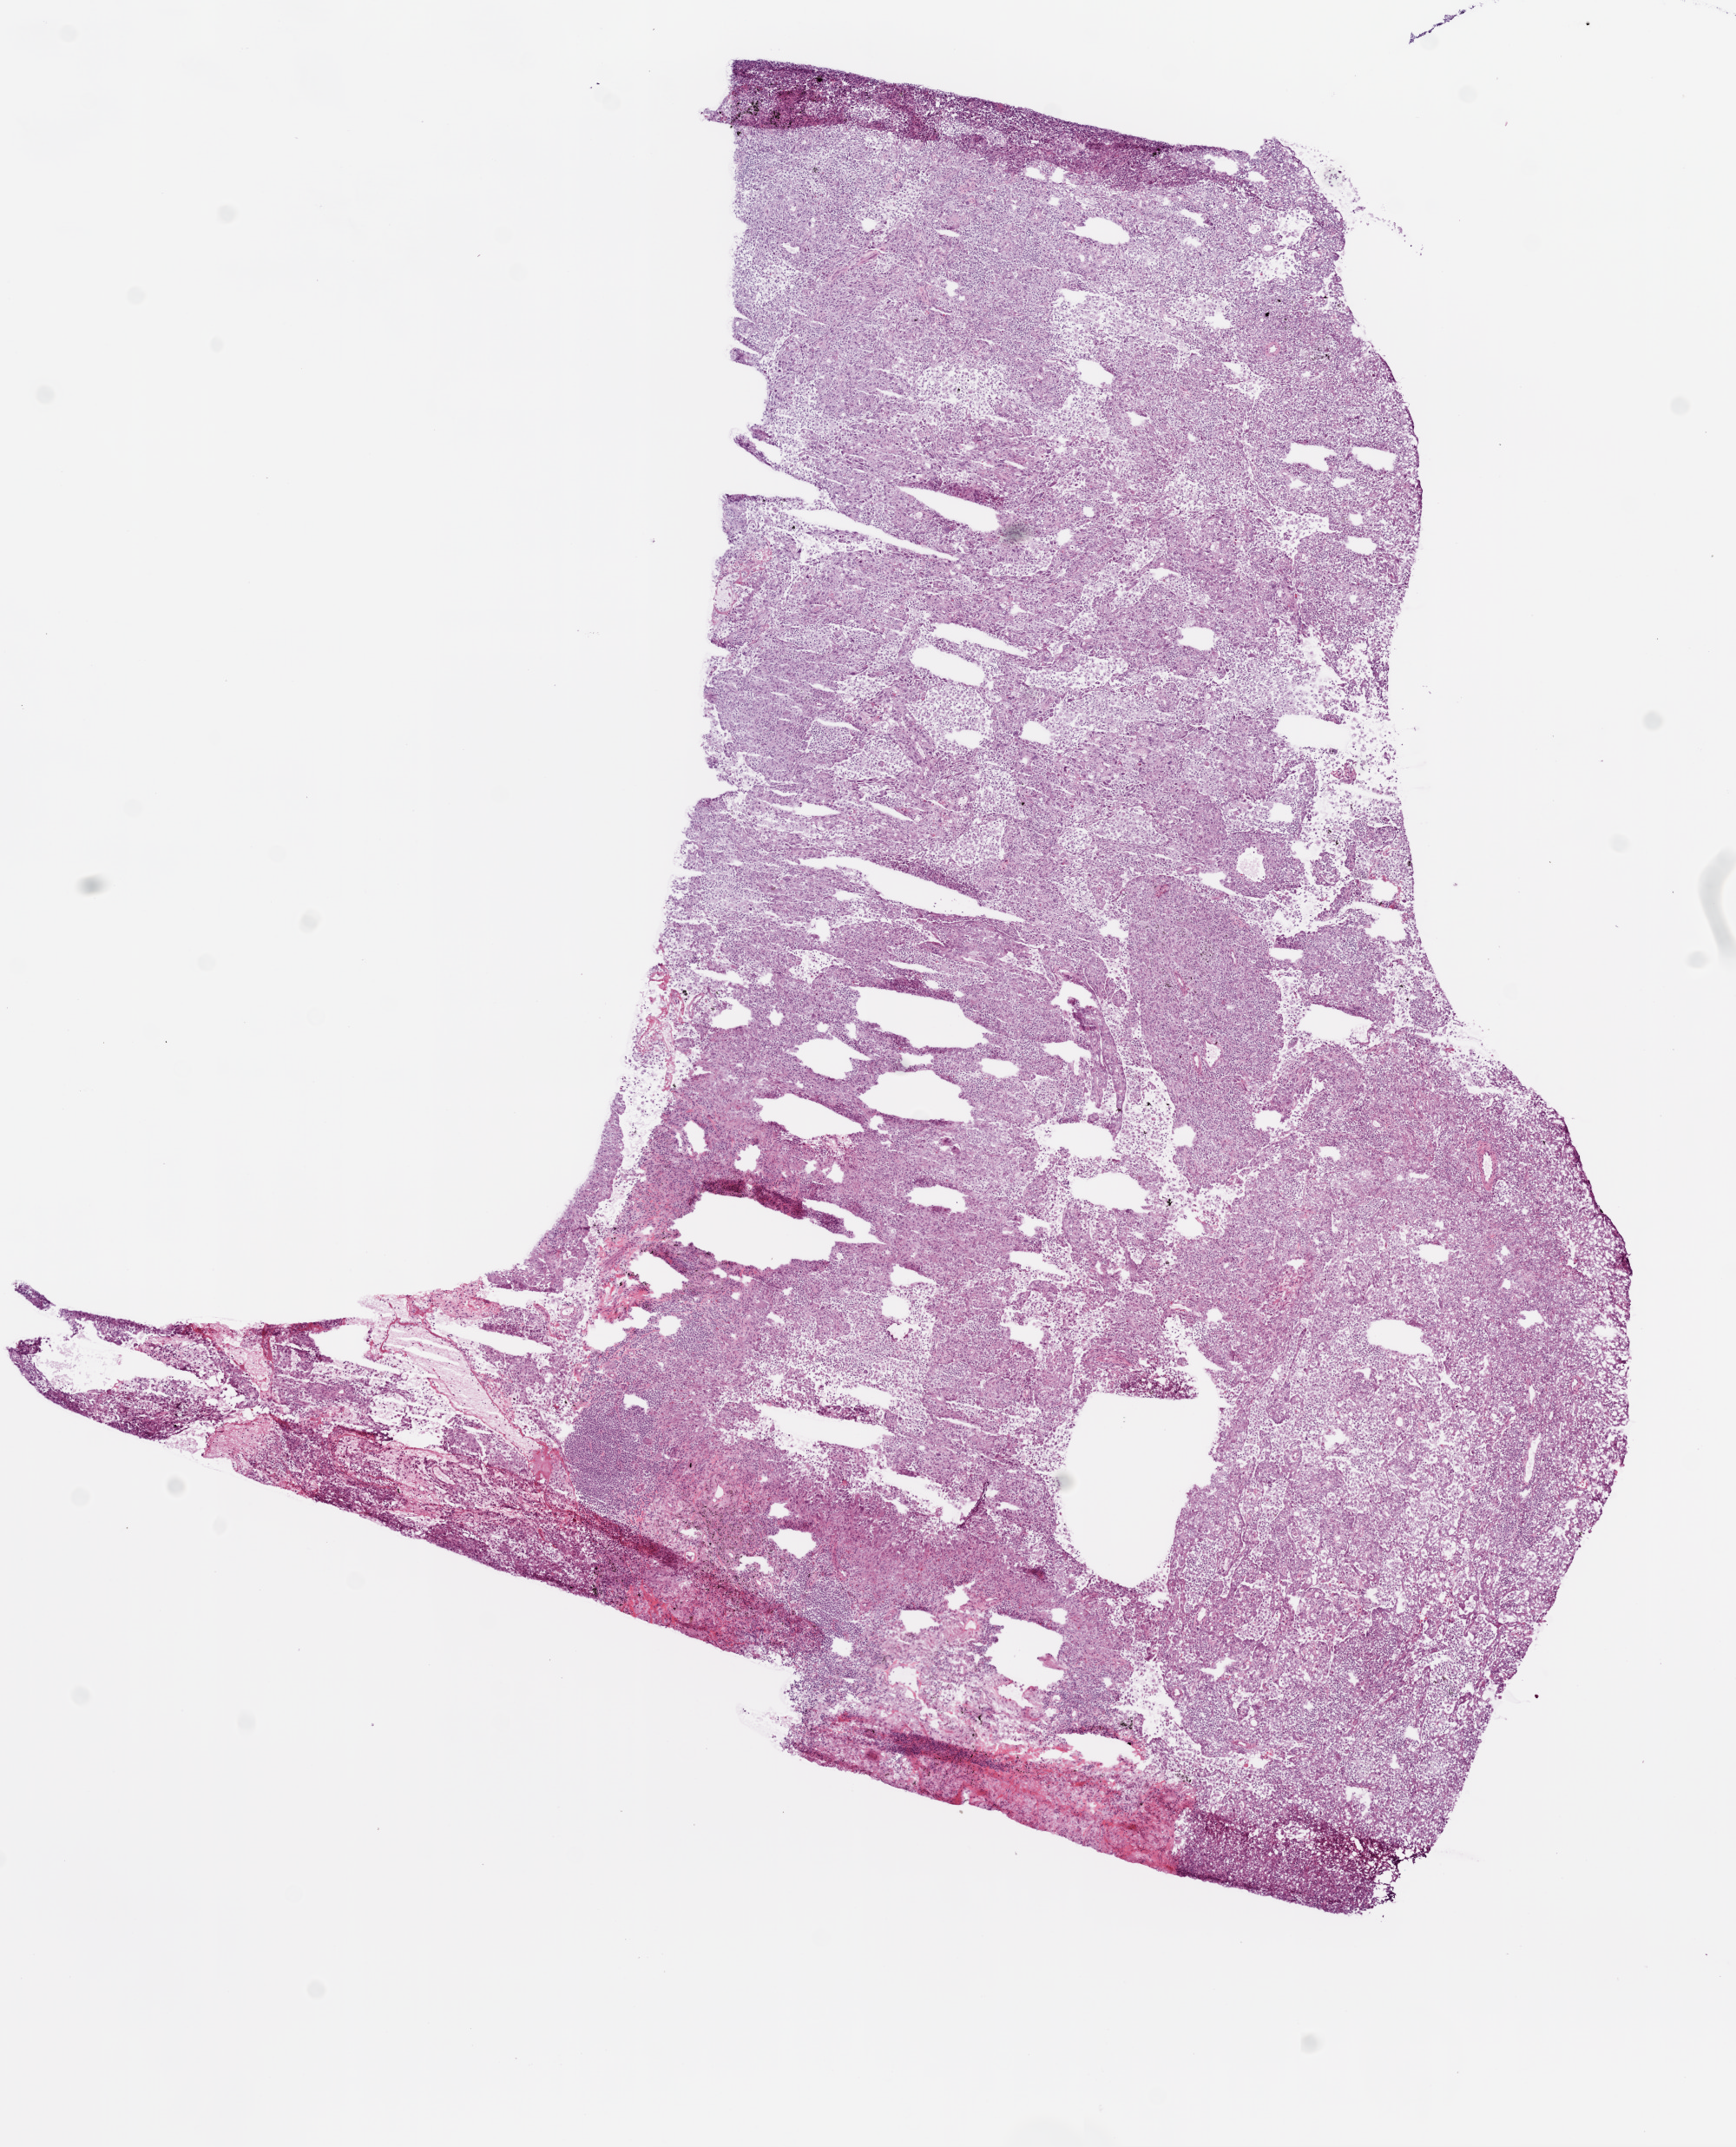
Whole-slide histology image, H&E-stained, whole scanned area (about 8.0 x 9.9 mm, from a 20x scan) shown as a low-resolution overview; frozen section from the bottom of the tissue portion; primary tumour sample from the lung. Male patient. Slide review estimates, as recorded: tumour cells 90%, tumour nuclei 65%, normal cells 0%, stromal cells 10%, necrosis 0%.
- histologic diagnosis: Adenocarcinoma, NOS (upper lobe, lung)
- laterality: left
- AJCC pathologic stage: IB